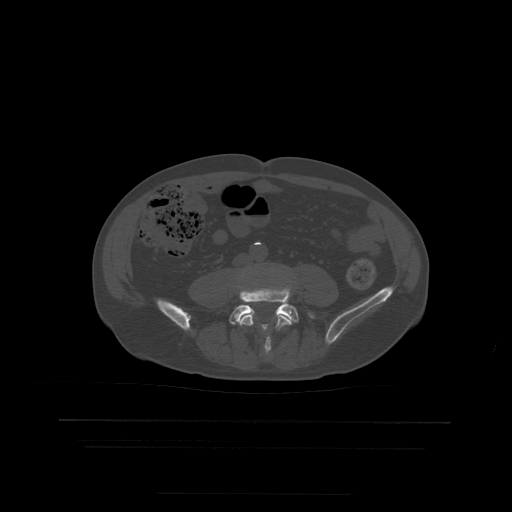
CT including the spine, one axial slice. Position 83 of 522 along the scan axis. Bone window (W 1800 / L 400 HU). 512 × 512 image matrix. Patient age 68 years. Case-level facts recorded for this patient, not image findings: primary cancer: urothelial.
Outlined on this slice (semi-automatically segmented with operator editing):
- L4 vertebra: bounding box [x1, y1, x2, y2] px = [239, 309, 292, 354]
- L5 vertebra: [229, 289, 315, 330]